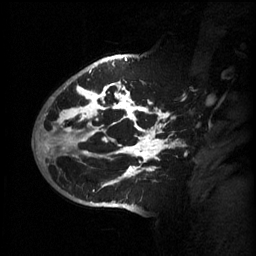
Breast MRI (dynamic contrast-enhanced), one sagittal slice. Slice 41 of 60 in the series (ordered by position). 3 images stored at this slice position (order not interpretable as contrast timing). 1.5 T. TE 4.2 ms, TR 11 ms. 2 mm slice thickness. 256 × 256 image matrix, field of view 220 × 220 mm. Female patient, age 51 years.
Annotated regions visible in this slice (semi-automatically segmented with operator editing):
- analysis volume of interest (the breast-tissue region the enhancement analysis was run in; not a lesion): bounding box [x1, y1, x2, y2] px = [63, 80, 186, 201]
- tumour enhancement mask (voxels above the 70 % enhancement threshold inside the analysis volume of interest): [63, 82, 181, 179]